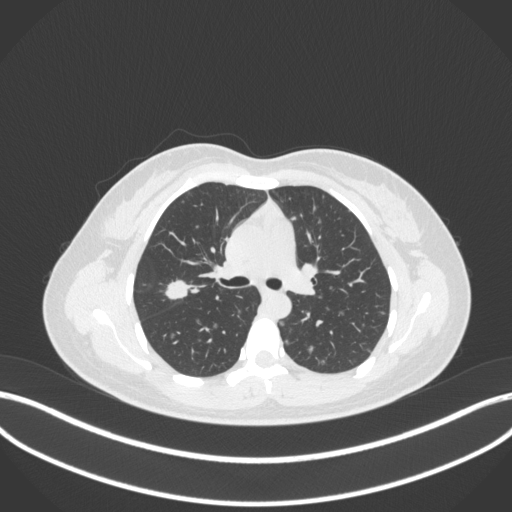
Chest CT, one axial slice; position 212 of 214 along the scan axis; 120 kVp; lung window (W 1500 / L -600 HU); 512 × 512 image matrix. Patient: female, 33 years. Case-level facts recorded for this patient, not image findings: clinical TNM (as recorded): T1c N0 M0.
Annotated regions visible in this slice (bounding box drawn by a radiologist):
- lung tumour (recorded histology: adenocarcinoma): bounding box <161,273,192,306> (left, top, right, bottom; pixels)